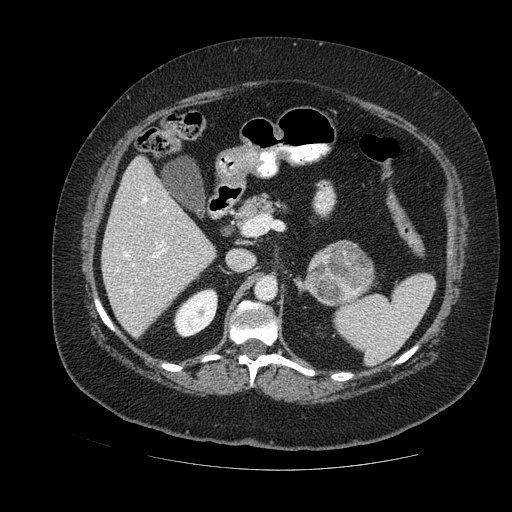
Contrast-enhanced abdominal CT, one axial slice; position 70 of 121 along the scan axis; soft-tissue window (W 400 / L 40 HU); 512 × 512 image matrix, field of view 420 × 420 mm. Female patient. From the clinical record (not read from this slice): diagnosis: adrenocortical carcinoma; tumour side: left adrenal.
Annotated regions visible in this slice (semi-automatically segmented with operator editing):
- mass: bounding box [x1, y1, x2, y2] px = [307, 242, 375, 303]